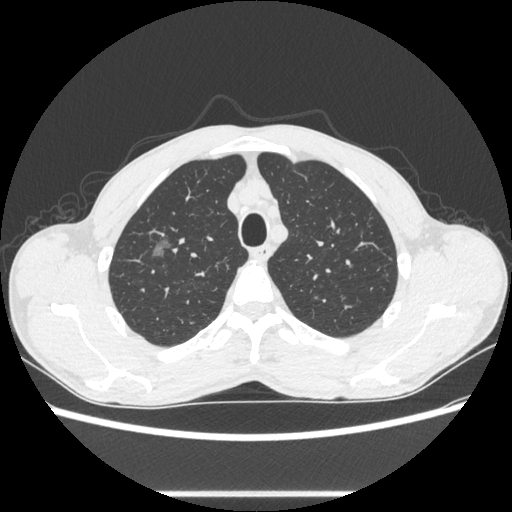
Chest CT, one axial slice; position 478 of 600 along the scan axis; reconstruction kernel STANDARD; lung window (W 1500 / L -600 HU); 0.62 mm slice thickness; 512 × 512 image matrix, field of view 357 × 357 mm. Male patient, age 54 years. From the clinical record (not read from this slice): clinical TNM (as recorded): T1a N0 M0.
Annotated regions visible in this slice (rectangle marked by the reading radiologist):
- lung tumour (recorded histology: adenocarcinoma): bounding box [x1, y1, x2, y2] px = [142, 233, 181, 265]